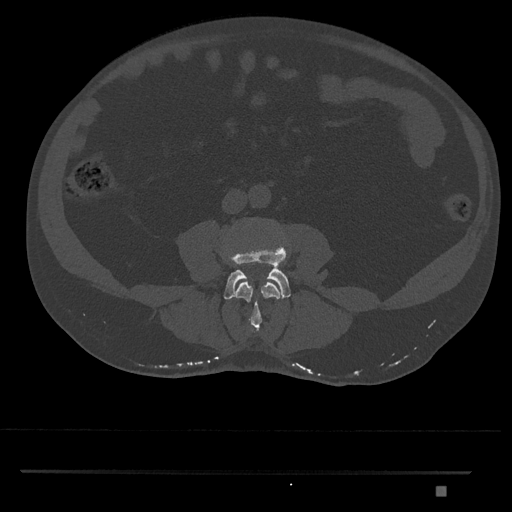
CT including the spine, one axial slice. Slice 645 of 1134 in the series (ordered by position). Reconstruction kernel Br40s/3. 120 kVp. Bone window (W 1800 / L 400 HU). 0.5 mm slice thickness. 512 × 512 image matrix, field of view 429 × 429 mm. Patient: male, 65 years. From the clinical record (not read from this slice): primary cancer: prostate.
Outlined on this slice (semi-automatic segmentation, software-assisted and operator-edited):
- L3 vertebra: bounding box (x1, y1, x2, y2) in pixels: (235, 282, 280, 333)
- L4 vertebra: (223, 236, 291, 300)